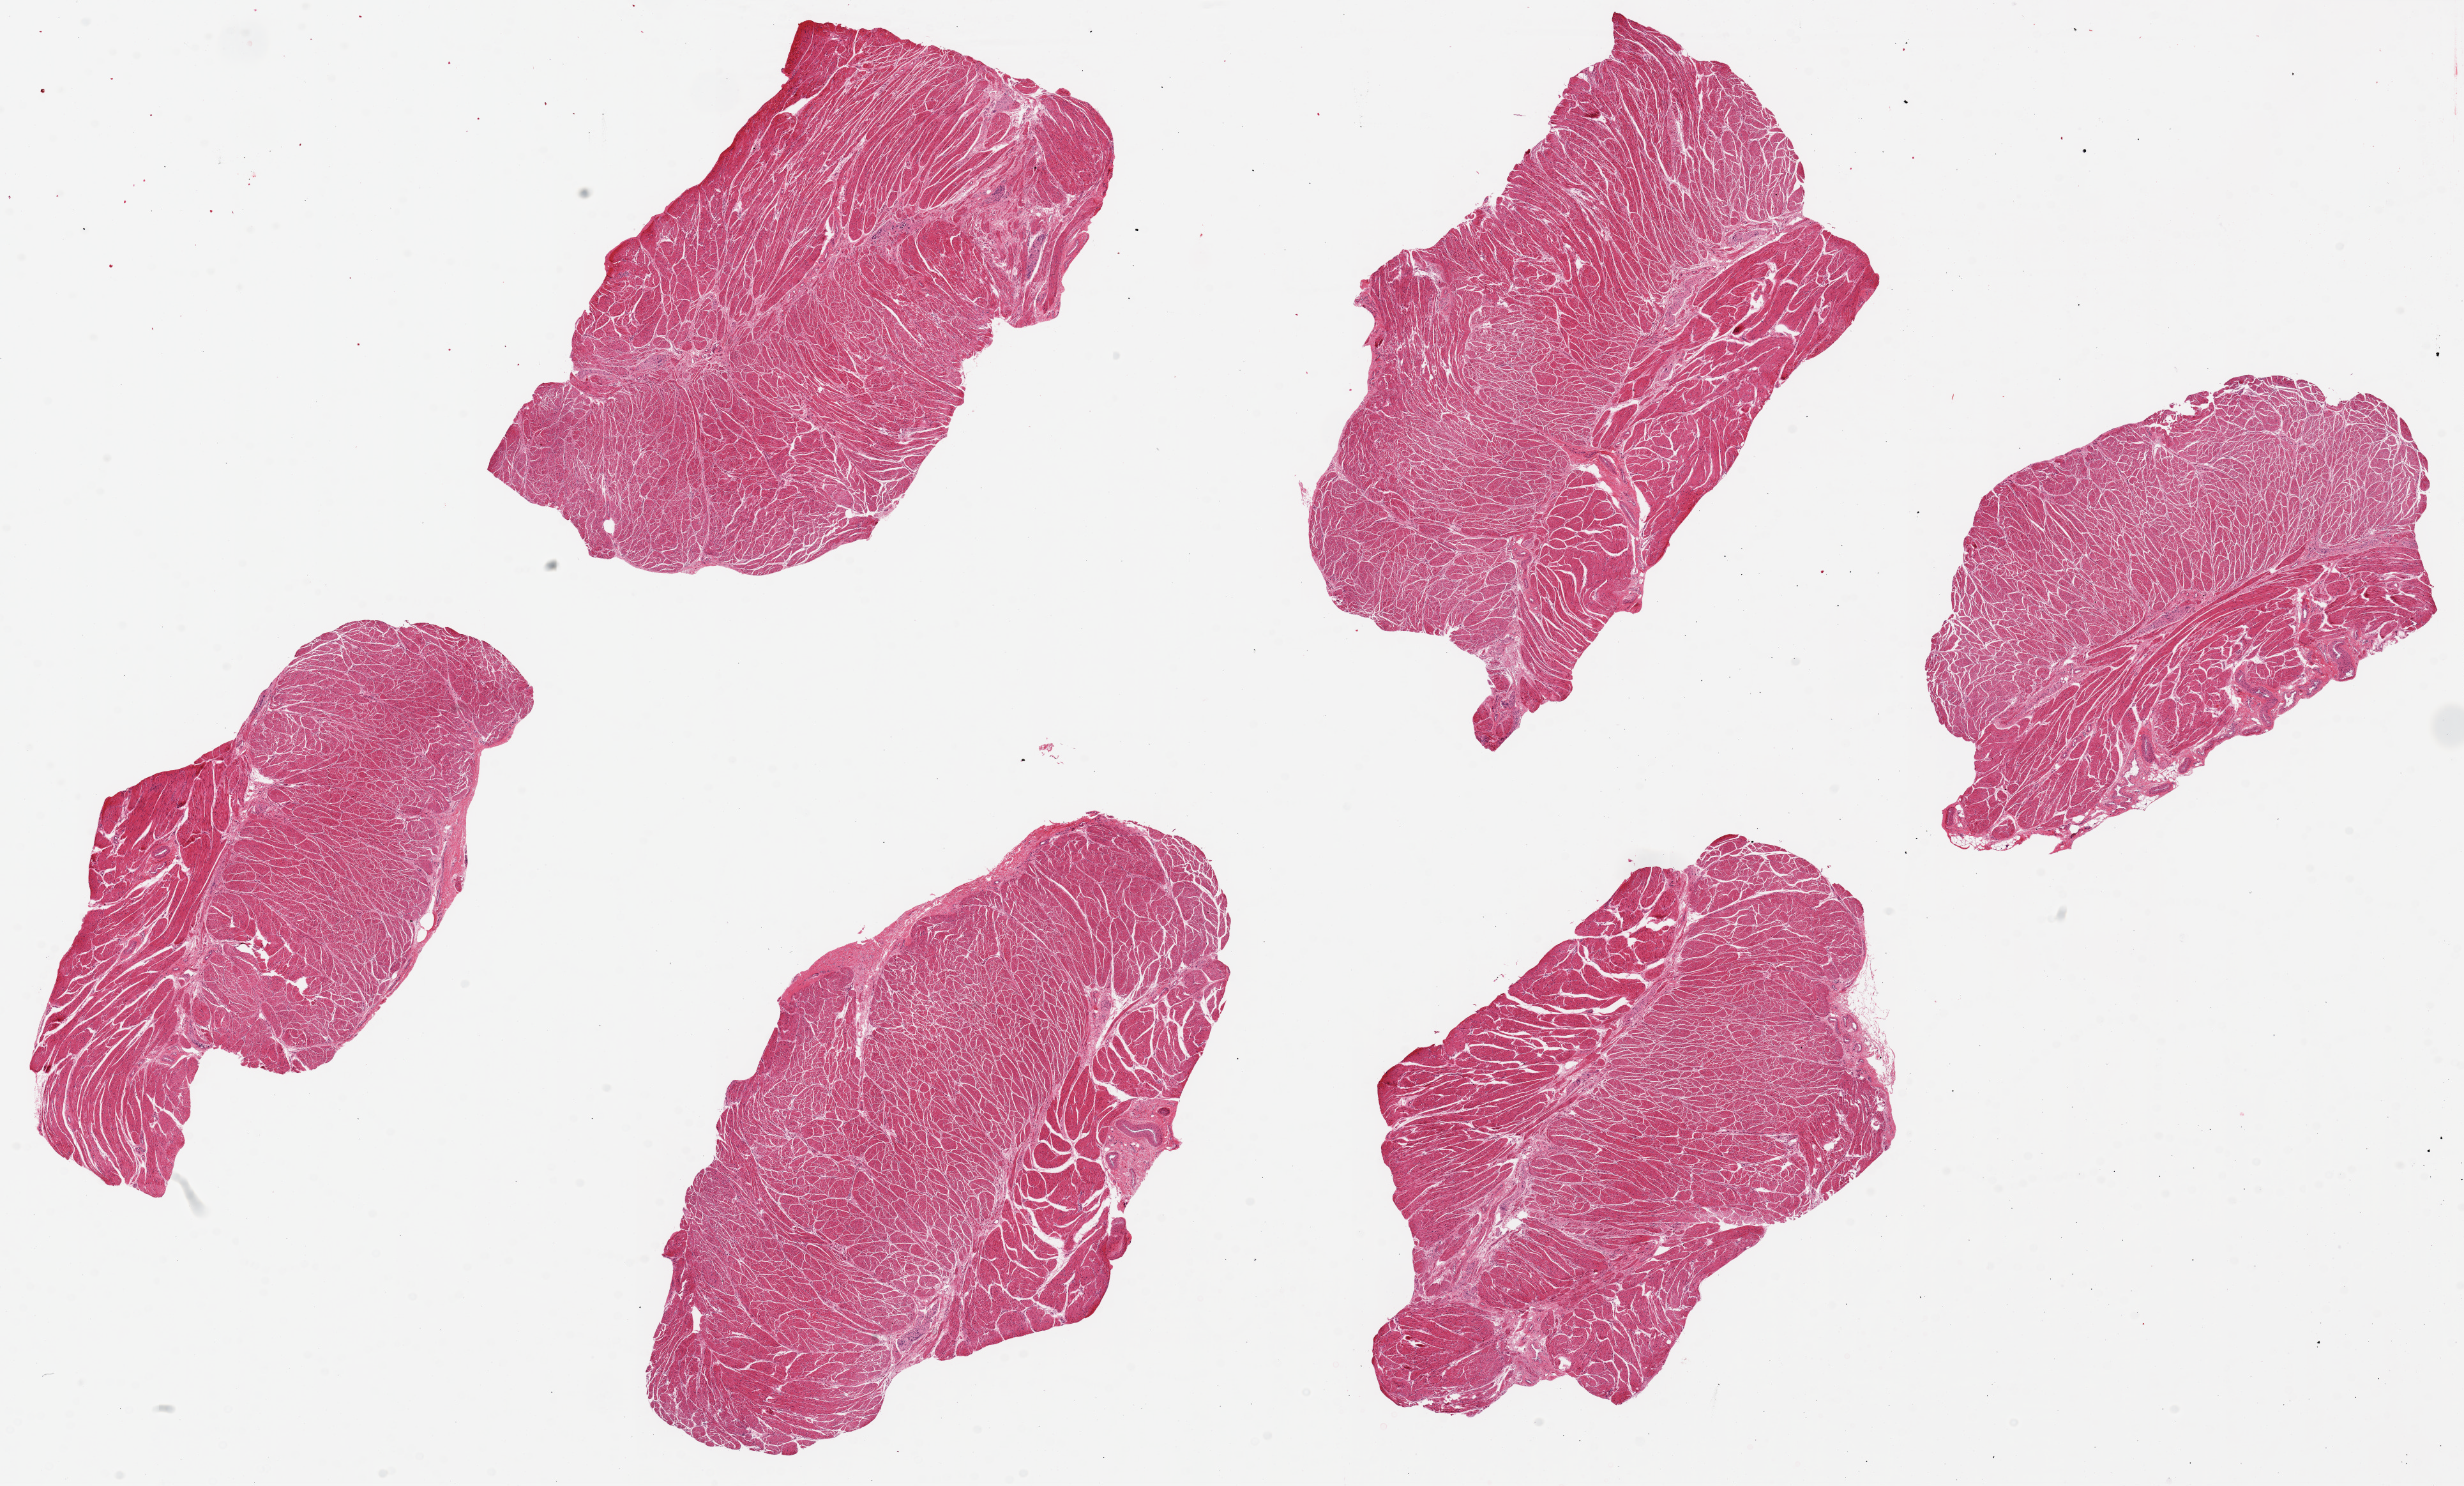
Digitized H&E-stained section, brightfield — shown as a low-resolution overview of the whole scanned area (about 30.5 x 18.4 mm); PAXgene-fixed paraffin-embedded (PFPE) section; sampled site (target tissue): esophageal muscle; donor tissue sample.
Review note (as recorded): 6 pieces, up to 10x6mm; Well sampled muscularis propria.